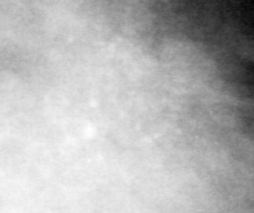
Region of interest cut from a scanned film mammogram (one marked finding), right breast, MLO view, BI-RADS breast density category 3 (scale 1–4).
- Mass, shape architectural distortion, margins spiculated; BI-RADS assessment category 5; subtlety rating 5 on a 1 (subtle) to 5 (obvious) scale; pathology (as recorded): malignant.